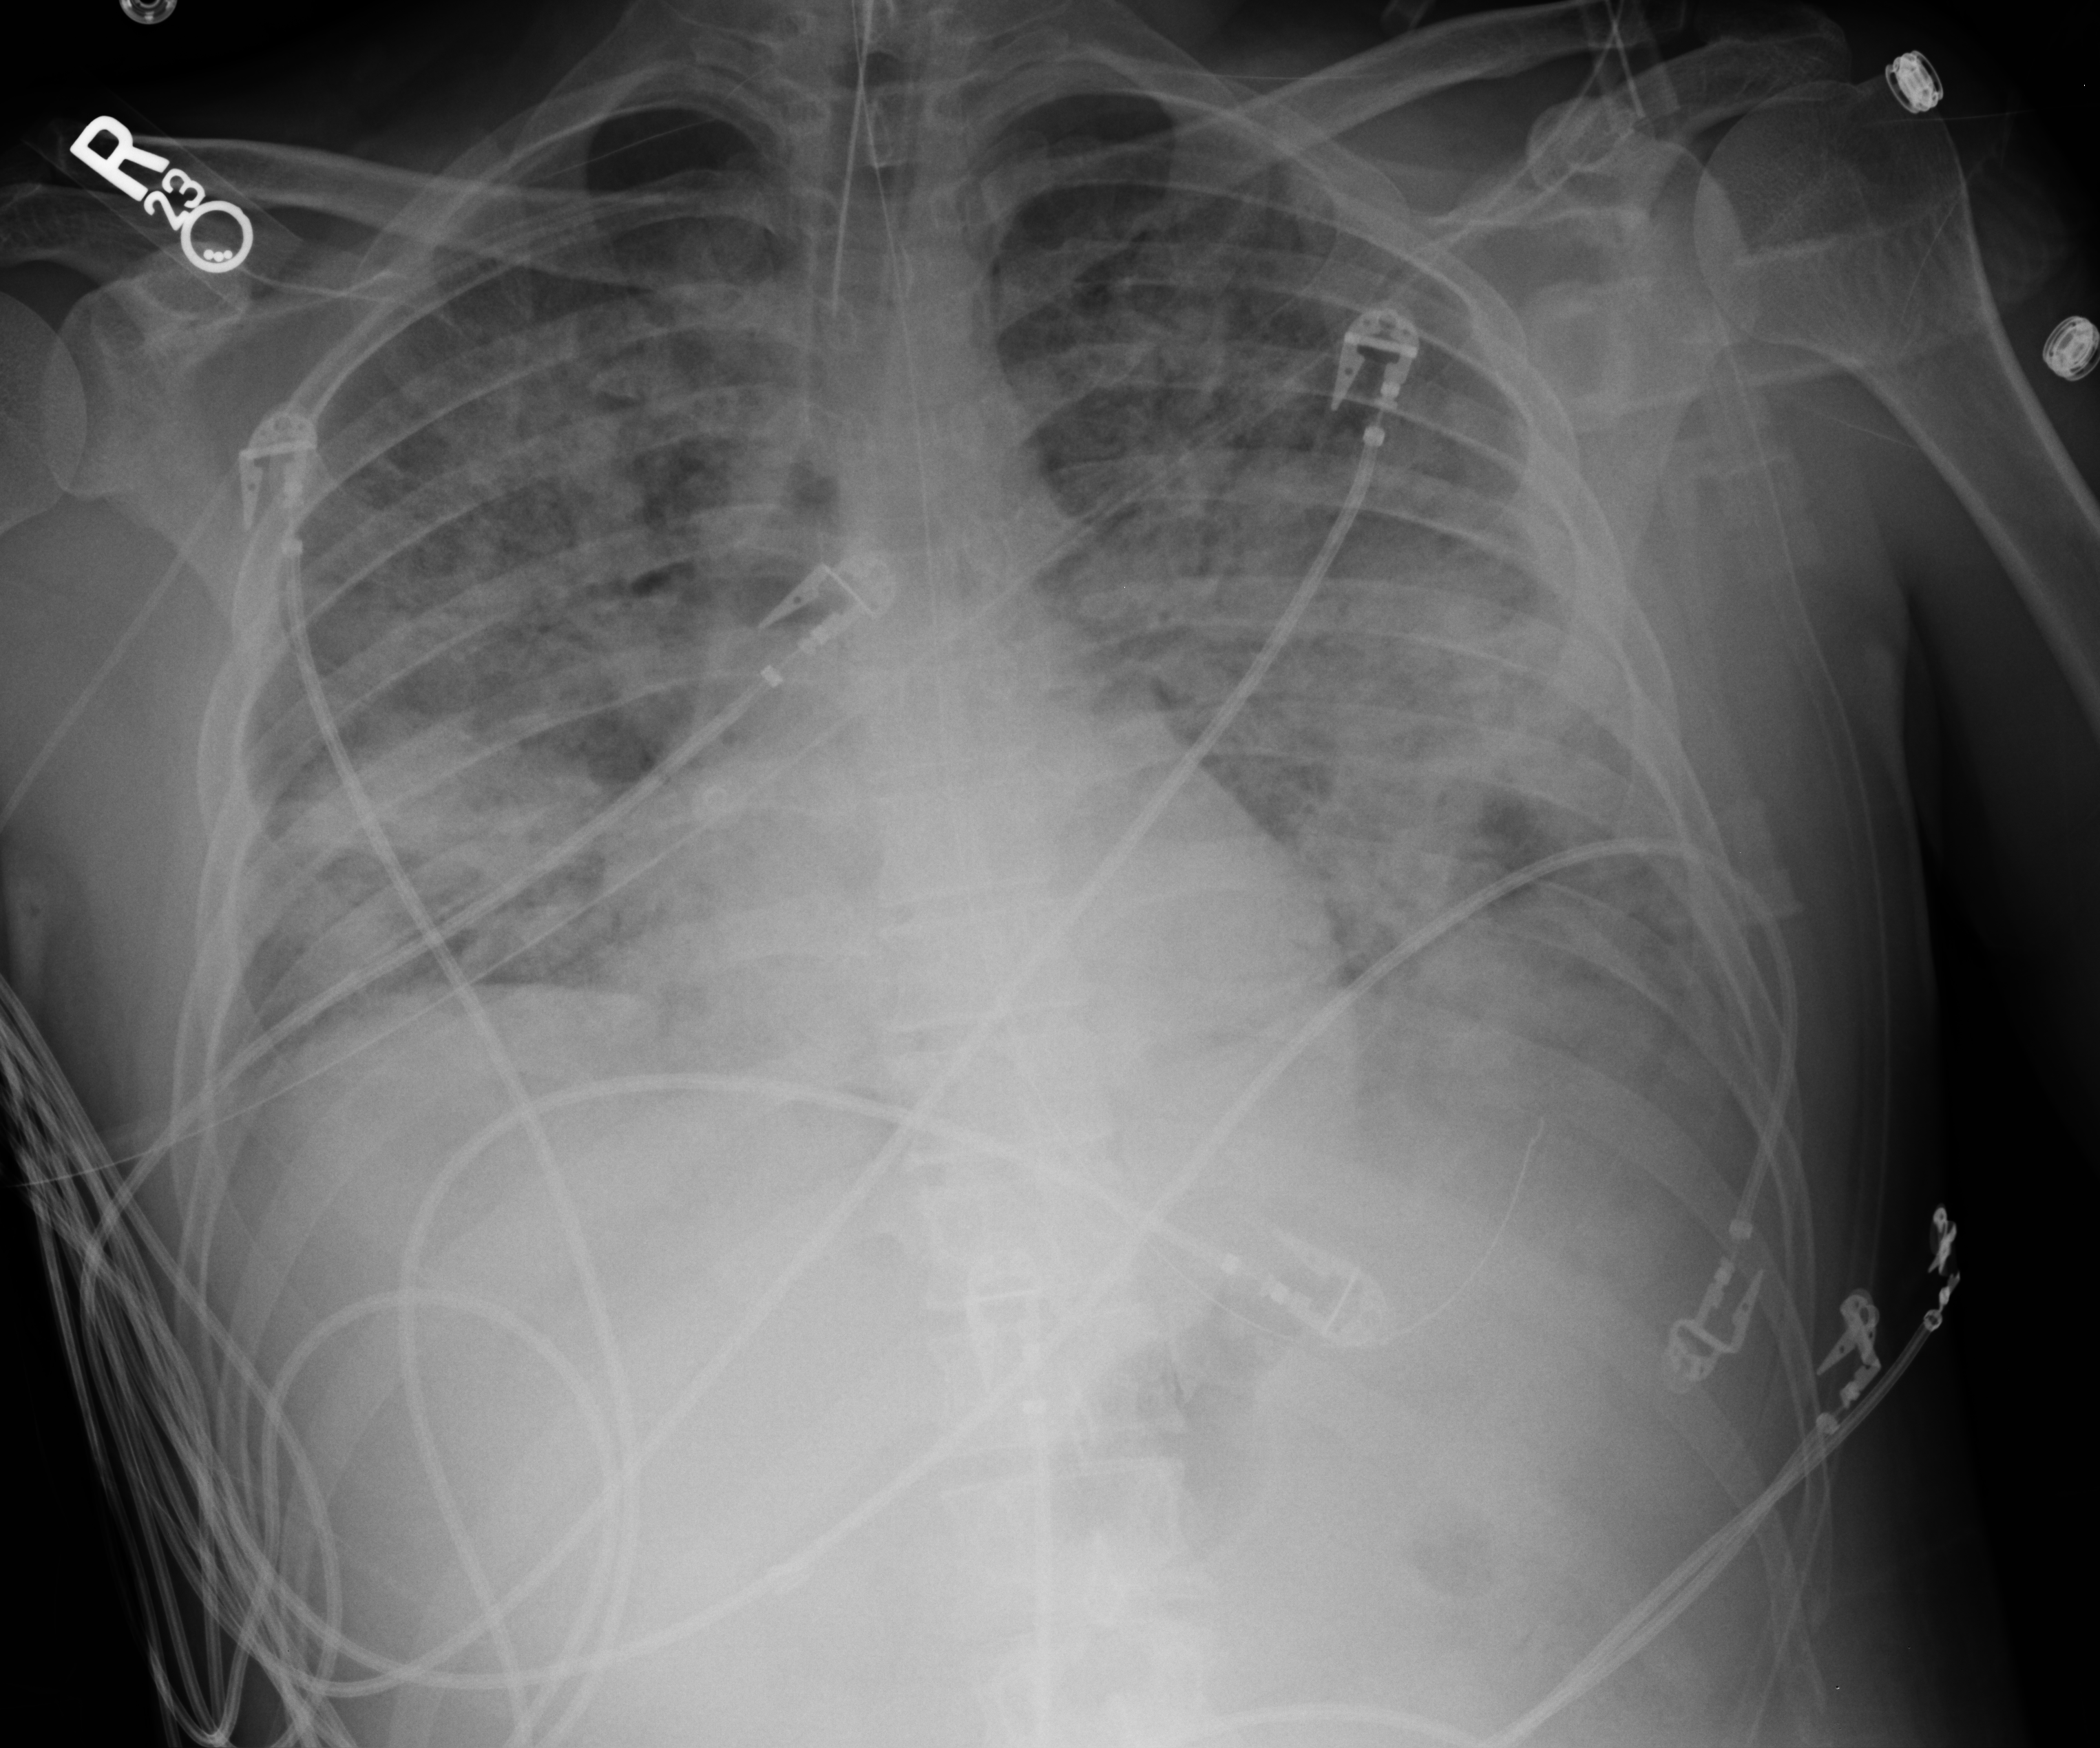
Chest X-ray (portable). Patient hospitalised with COVID-19; male, aged 18–59 years.
Admission-level facts for this patient (not findings on this image; timing relative to this image not recorded):
- mechanically ventilated during this hospital stay: yes
- admitted to intensive care during this hospital stay: yes
- length of hospital stay: 29 days